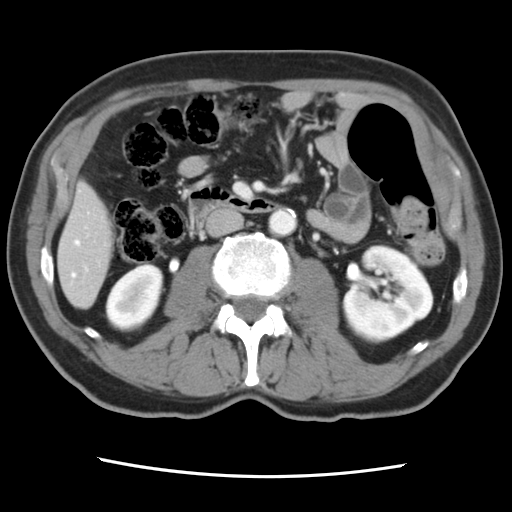
Contrast-enhanced abdominal CT, one axial slice. Slice 24 of 83 in the series (ordered by position). 120 kVp. Intravenous contrast given. Soft-tissue window (W 400 / L 40 HU). 5 mm slice thickness. 512 × 512 image matrix. Male patient, age 69 years. Case-level facts recorded for this patient, not image findings: diagnosis: colorectal cancer liver metastases, imaged before liver resection; multiple liver metastases: yes; largest metastasis: 3.5 cm; chemotherapy before resection: yes.
Annotated regions visible in this slice (outlined manually by an expert reader):
- hepatic veins: box from (x=72, y=240) to (x=80, y=277) px
- liver: (x=59, y=186)–(x=112, y=307)
- planned liver remnant (the part of the liver to remain after resection): (x=59, y=185)–(x=113, y=307)